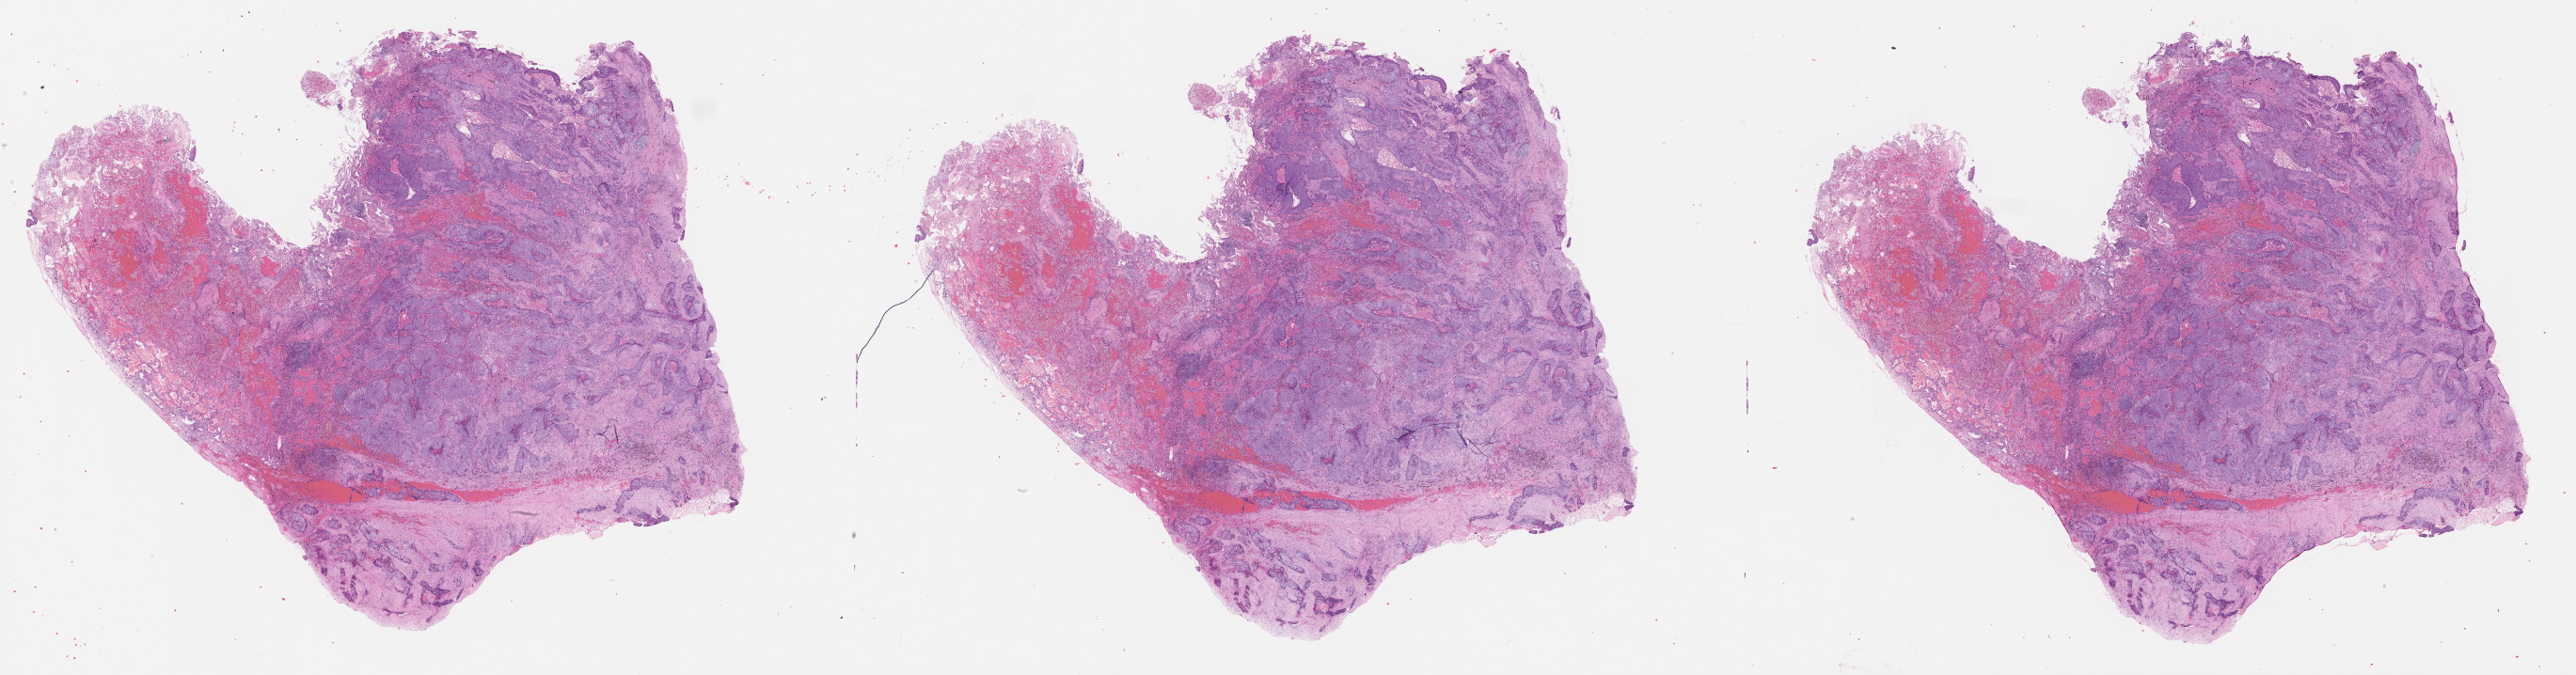
Digitized H&E-stained tissue section (whole slide) — a low-resolution overview of the entire scanned area, about 44.1 x 11.6 mm, tumour tissue sample, lung. 57-year-old male patient.
* patient diagnosis (cohort enrolment): squamous cell carcinoma (lung)